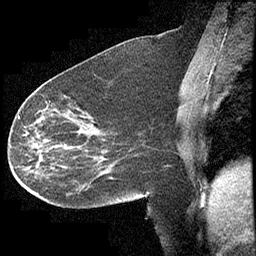
Breast MRI (dynamic contrast-enhanced), one sagittal slice; slice 174 of 232 in the series (ordered by position); dynamic contrast-enhanced study with each time point stored as its own series, time point 2 of 4 at this slice position (early post-contrast, ordered by acquisition time); 1.5 T; TE 4.2 ms, TR 6.7 ms; 3 mm slice thickness; 256 × 256 image matrix, field of view 200 × 200 mm. Female patient, age 63 years. Case-level facts recorded for this patient, not image findings: setting: breast cancer imaged before/during neoadjuvant chemotherapy; receptor status: triple-negative.
Annotated regions visible in this slice (semi-automatically segmented with operator editing):
- analysis volume of interest (the breast-tissue region the enhancement analysis was run in; not a lesion): bounding box <13,90,140,209> (left, top, right, bottom; pixels)
- tumour enhancement mask (voxels above the 70 % enhancement threshold inside the analysis volume of interest): <18,116,40,168>